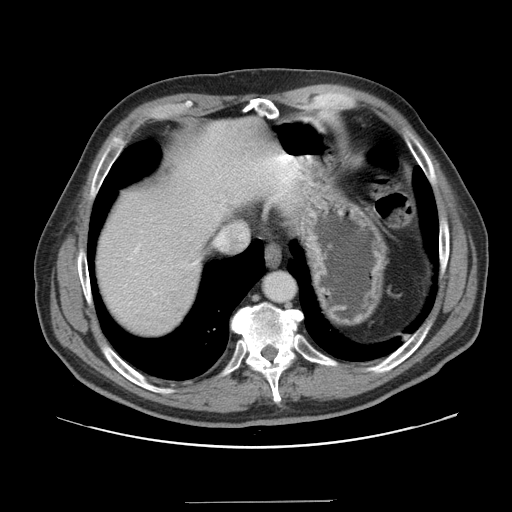
Contrast-enhanced abdominal CT, one axial slice; slice 136 of 151 in the series (ordered by position); 120 kVp; intravenous contrast given; soft-tissue window (W 400 / L 40 HU); 512 × 512 image matrix, field of view 399 × 399 mm. Male patient, age 63 years. Case-level facts recorded for this patient, not image findings: diagnosis: colorectal cancer liver metastases, imaged before liver resection; multiple liver metastases: no; largest metastasis: 2.1 cm.
Annotated regions visible in this slice (expert manual segmentation):
- hepatic veins: bounding box [x1, y1, x2, y2] px = [219, 236, 224, 243]
- liver: [95, 117, 300, 337]
- planned liver remnant (the part of the liver to remain after resection): [95, 144, 231, 337]